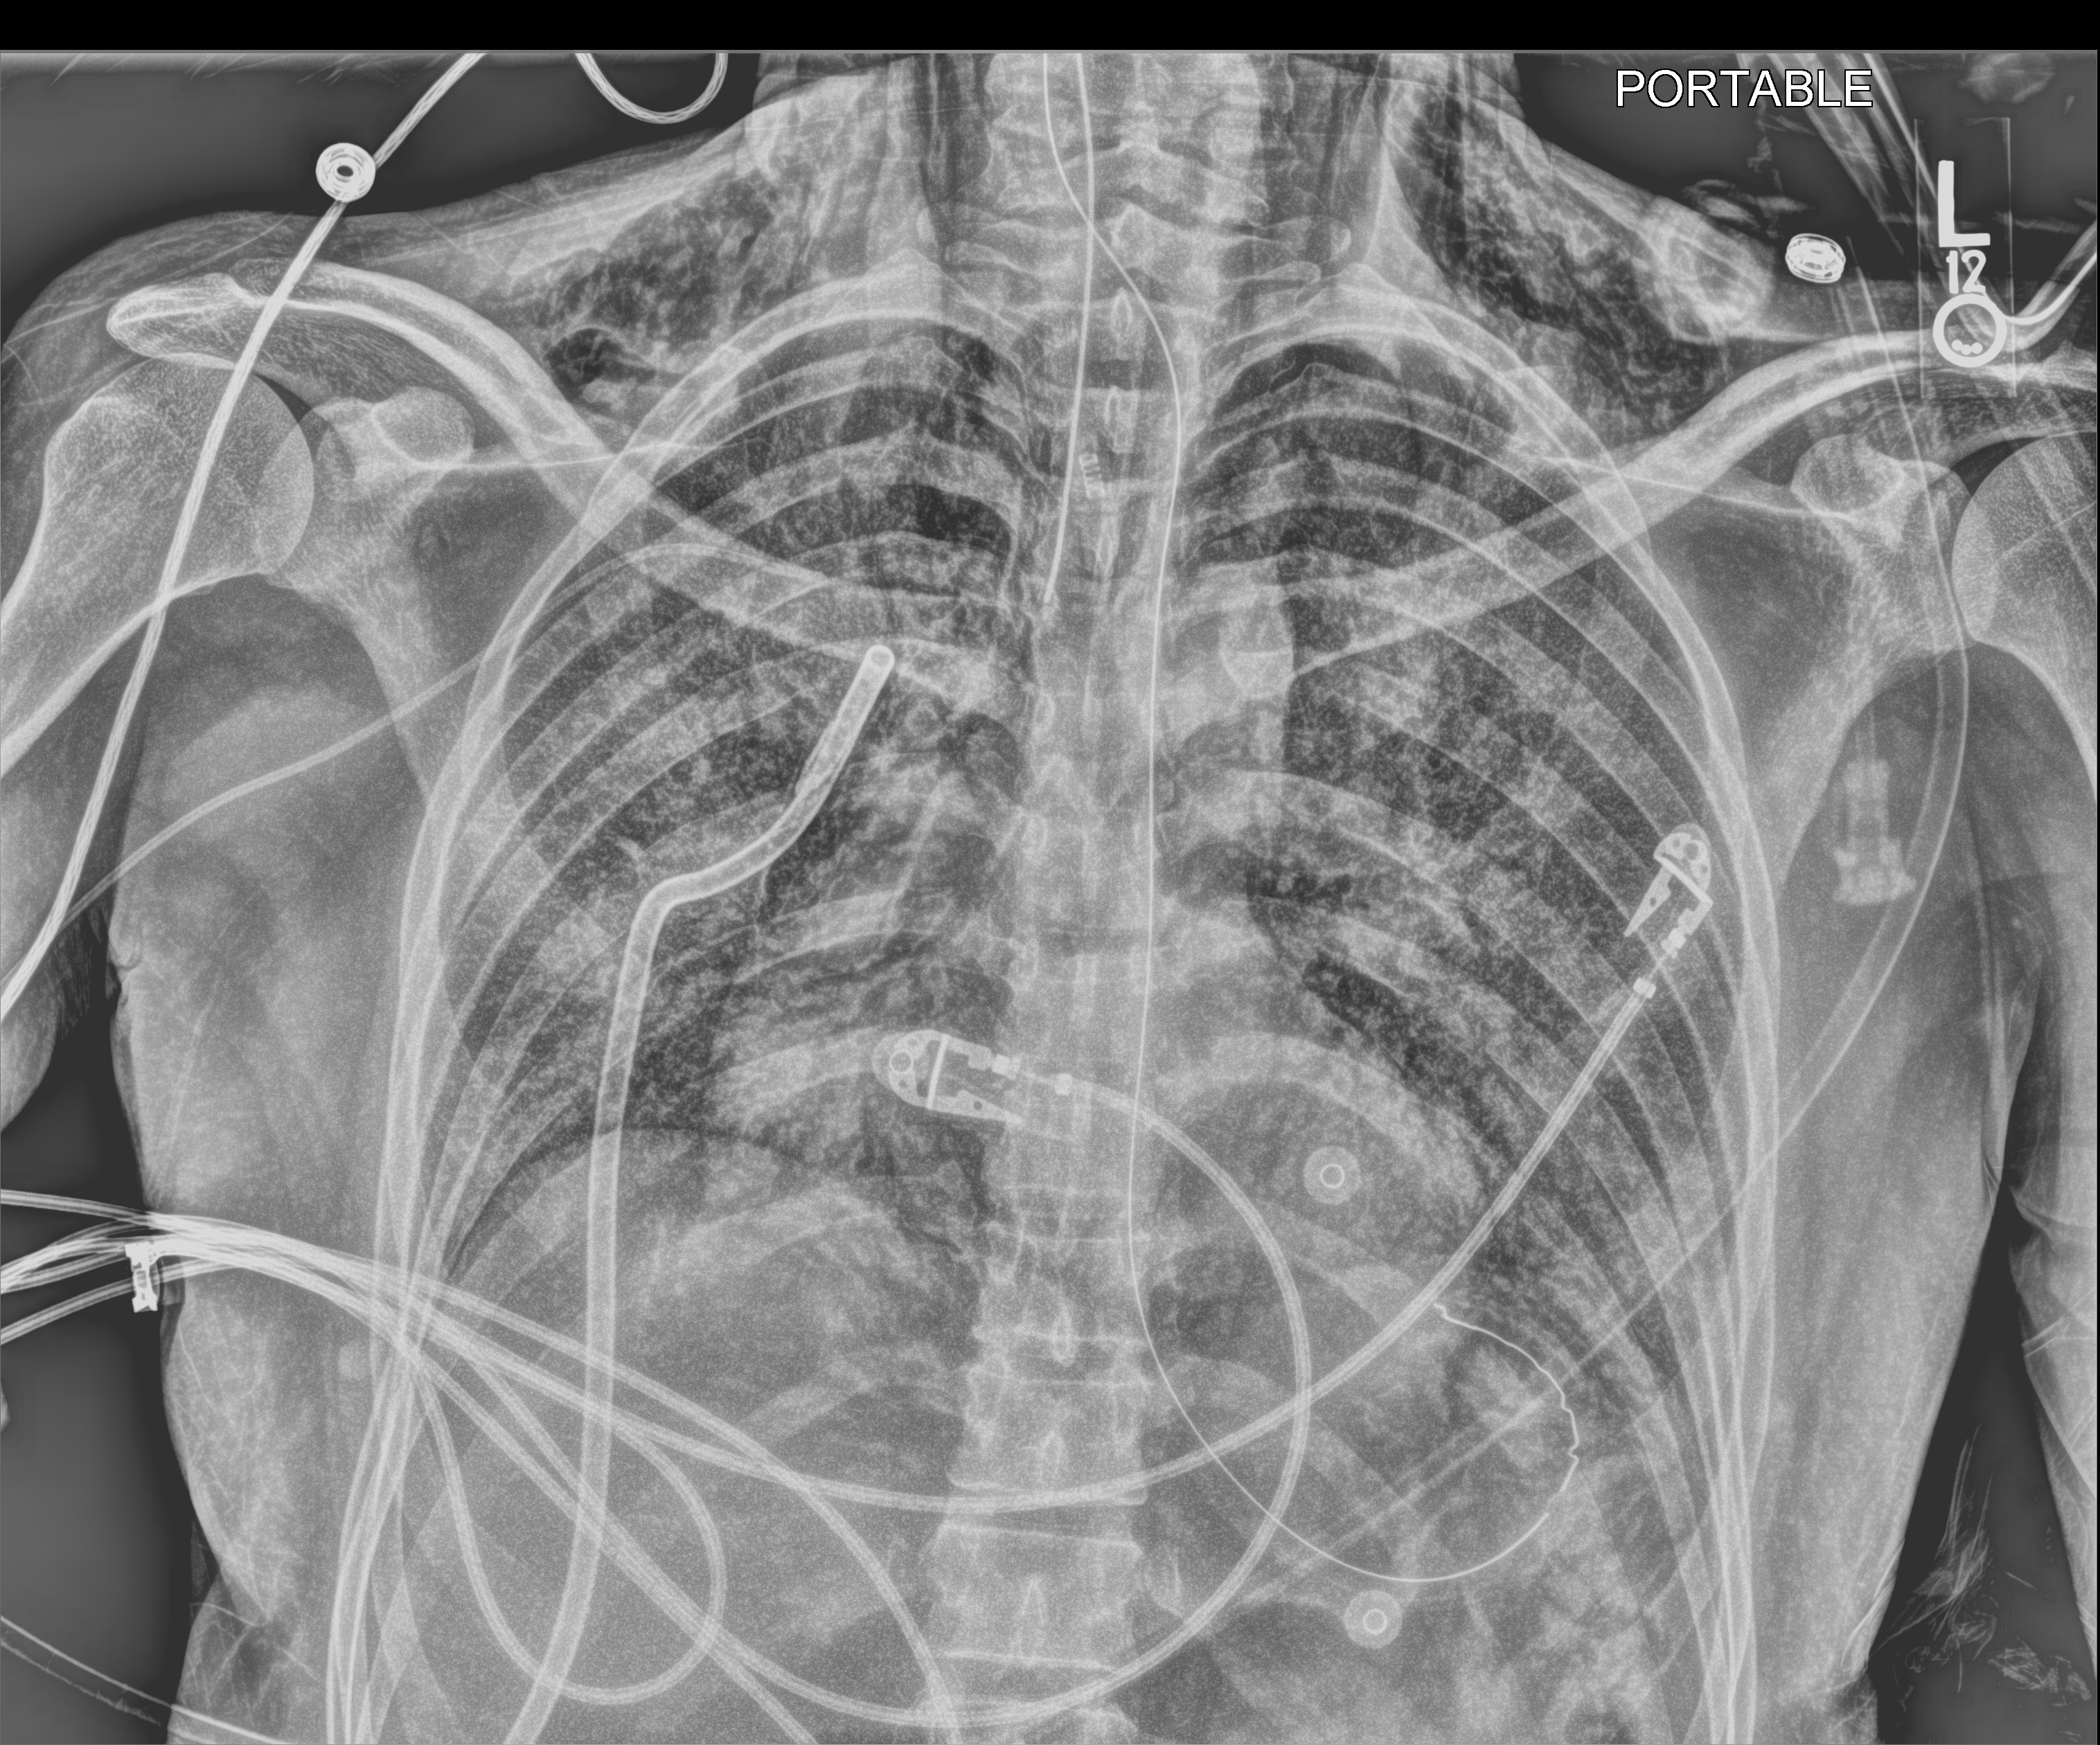
Chest X-ray (portable); anteroposterior (AP) projection. Adult patient hospitalised with COVID-19, age 18–59 years.
Hospital-stay facts (about this admission, not read from this image; timing relative to this image not recorded): mechanically ventilated during this hospital stay: yes; length of hospital stay: 41 days; chronic kidney disease (admission record): no.